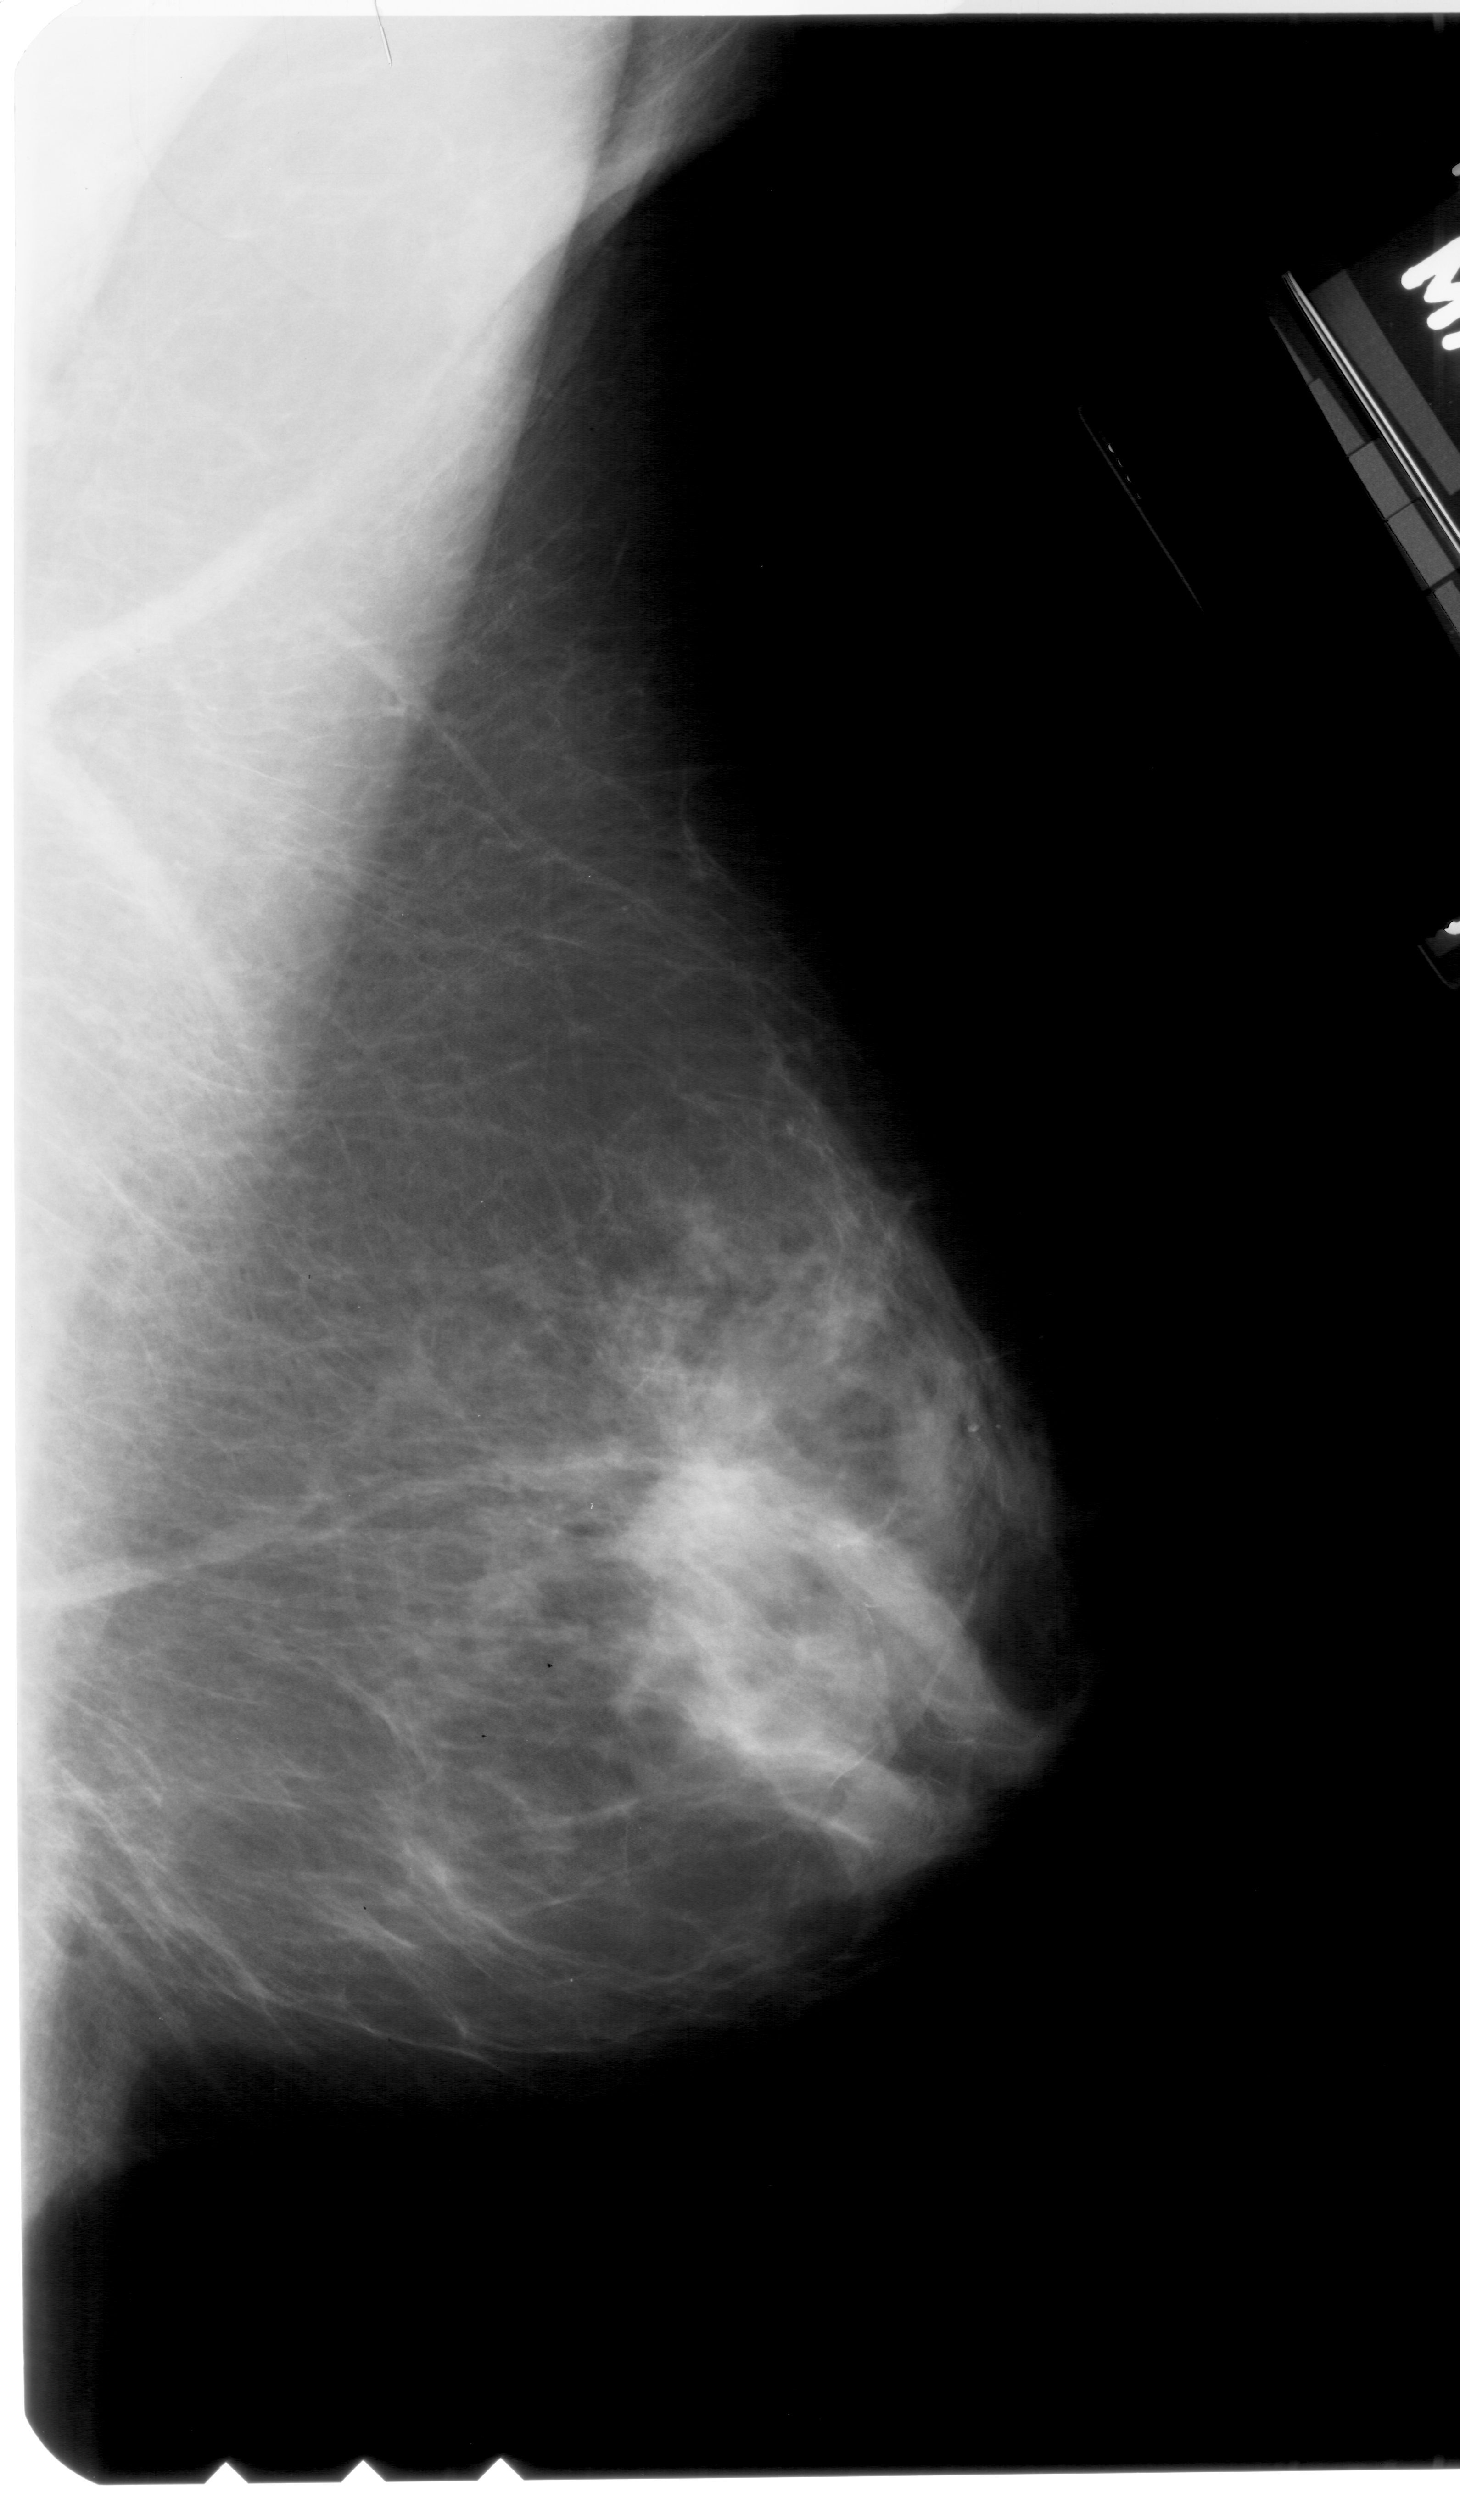
Mammogram (digitized film), right breast, MLO view, BI-RADS breast density category 3 (scale 1–4).
Abnormality record for this image: mass, shape irregular, margins ill defined; BI-RADS assessment category 4; subtlety rating 3 on a 1 (subtle) to 5 (obvious) scale; pathology (as recorded): malignant.